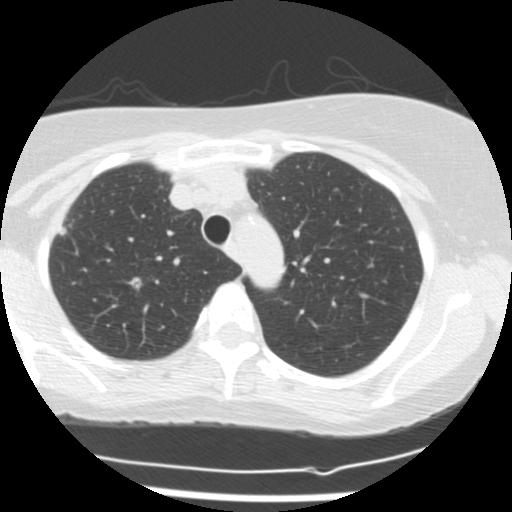
Low-dose screening chest CT, axial slice, first (baseline) screen, lung window (W 1500 / L -600 HU), 2.5 mm slice thickness, standard (soft-tissue) reconstruction kernel (STANDARD). Female, age 58 years at enrolment. Former smoker at enrolment.
Expert reader's lesion annotation, bounding box <44,207,87,245> (left, top, right, bottom; pixels). Screening reader's record for this exam (one nodule recorded; not confirmed to be the boxed lesion): non-calcified nodule or mass ≥4 mm, right upper lobe, 12 × 9 mm, spiculated (stellate) margins, soft tissue attenuation. Later outcome: lung cancer diagnosed 21 days after this screen — adenocarcinoma, NOS, right upper lobe, moderately differentiated (G2), stage IA (AJCC 6th edition), 10 mm at pathology.